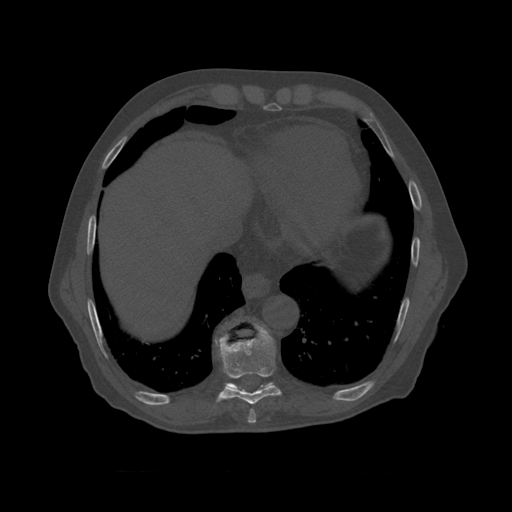
CT including the spine, one axial slice; slice 442 of 450 in the series (ordered by position); reconstruction kernel STANDARD; 120 kVp; bone window (W 1800 / L 400 HU); 1.25 mm slice thickness; 512 × 512 image matrix. Patient age 75 years. From the clinical record (not read from this slice): primary cancer: prostate.
Outlined on this slice (semi-automatically segmented with operator editing):
- T8 vertebra: bounding box (x1, y1, x2, y2) in pixels: (215, 321, 282, 410)
- T9 vertebra: (225, 323, 274, 390)